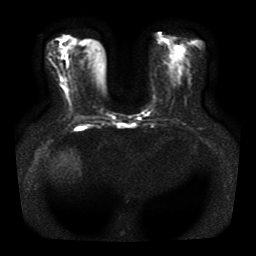
Breast MRI, one axial slice; slice 20 of 41 in the series (ordered by position); diffusion-weighted series; image 2 of 4 stored at this slice position (different b-values; order by instance number); 1.5 T; 5 mm slice thickness; 256 × 256 image matrix, field of view 330 × 330 mm. Female patient.
Annotated regions visible in this slice (expert manual segmentation):
- tumour on diffusion-weighted imaging: bounding box (x1, y1, x2, y2) in pixels: (64, 87, 67, 91)